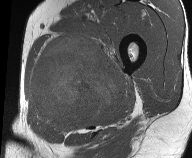
MRI of an extremity soft-tissue mass, one axial slice; slice 28 of 61 in the series (ordered by position); MR volume resampled by the dataset authors to the PET/CT grid (not the native acquisition matrix); 3.27 mm slice thickness; 192 × 158 image matrix, field of view 187 × 154 mm. Male patient. From the clinical record (not read from this slice): histological type: pleiomorphic liposarcoma; grade: high; site of the primary tumour: left thigh.
Annotated regions visible in this slice (expert contour drawn on MRI and transferred to this co-registered scan by the dataset authors):
- gross tumour volume including surrounding oedema: box from (x=27, y=32) to (x=128, y=131) px
- gross tumour volume (mass): (x=32, y=37)–(x=122, y=125)